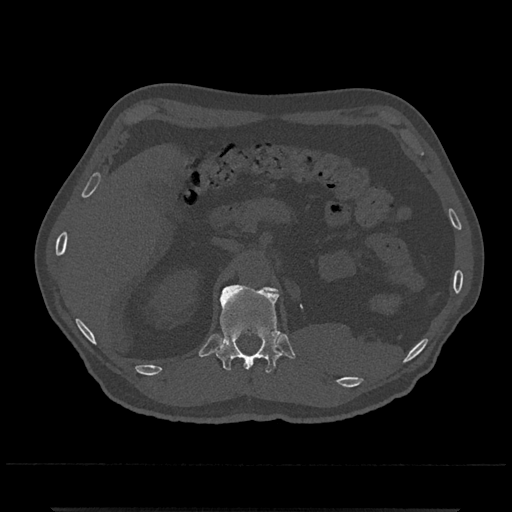
CT including the spine, one axial slice; slice 429 of 797 in the series (ordered by position); reconstruction kernel Br40s/3; 120 kVp; bone window (W 1800 / L 400 HU); 0.5 mm slice thickness; 512 × 512 image matrix, field of view 393 × 393 mm. Male patient, age 67 years. Case-level facts recorded for this patient, not image findings: primary cancer: prostate.
Structures marked on this image (semi-automatically segmented with operator editing):
- T12 vertebra: bounding box (x1, y1, x2, y2) in pixels: (214, 284, 282, 373)